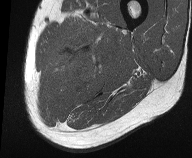
MRI of an extremity soft-tissue mass, one axial slice. Position 14 of 61 along the scan axis. MR volume resampled by the dataset authors to the PET/CT grid (not the native acquisition matrix). 3.27 mm slice thickness. 192 × 158 image matrix. Male patient. From the clinical record (not read from this slice): histological type: pleiomorphic liposarcoma; grade: high; site of the primary tumour: left thigh.
Structures marked on this image (expert contour drawn on MRI and transferred to this co-registered scan by the dataset authors):
- gross tumour volume including surrounding oedema: box from (x=52, y=16) to (x=119, y=90) px
- gross tumour volume (mass): (x=64, y=60)–(x=99, y=84)